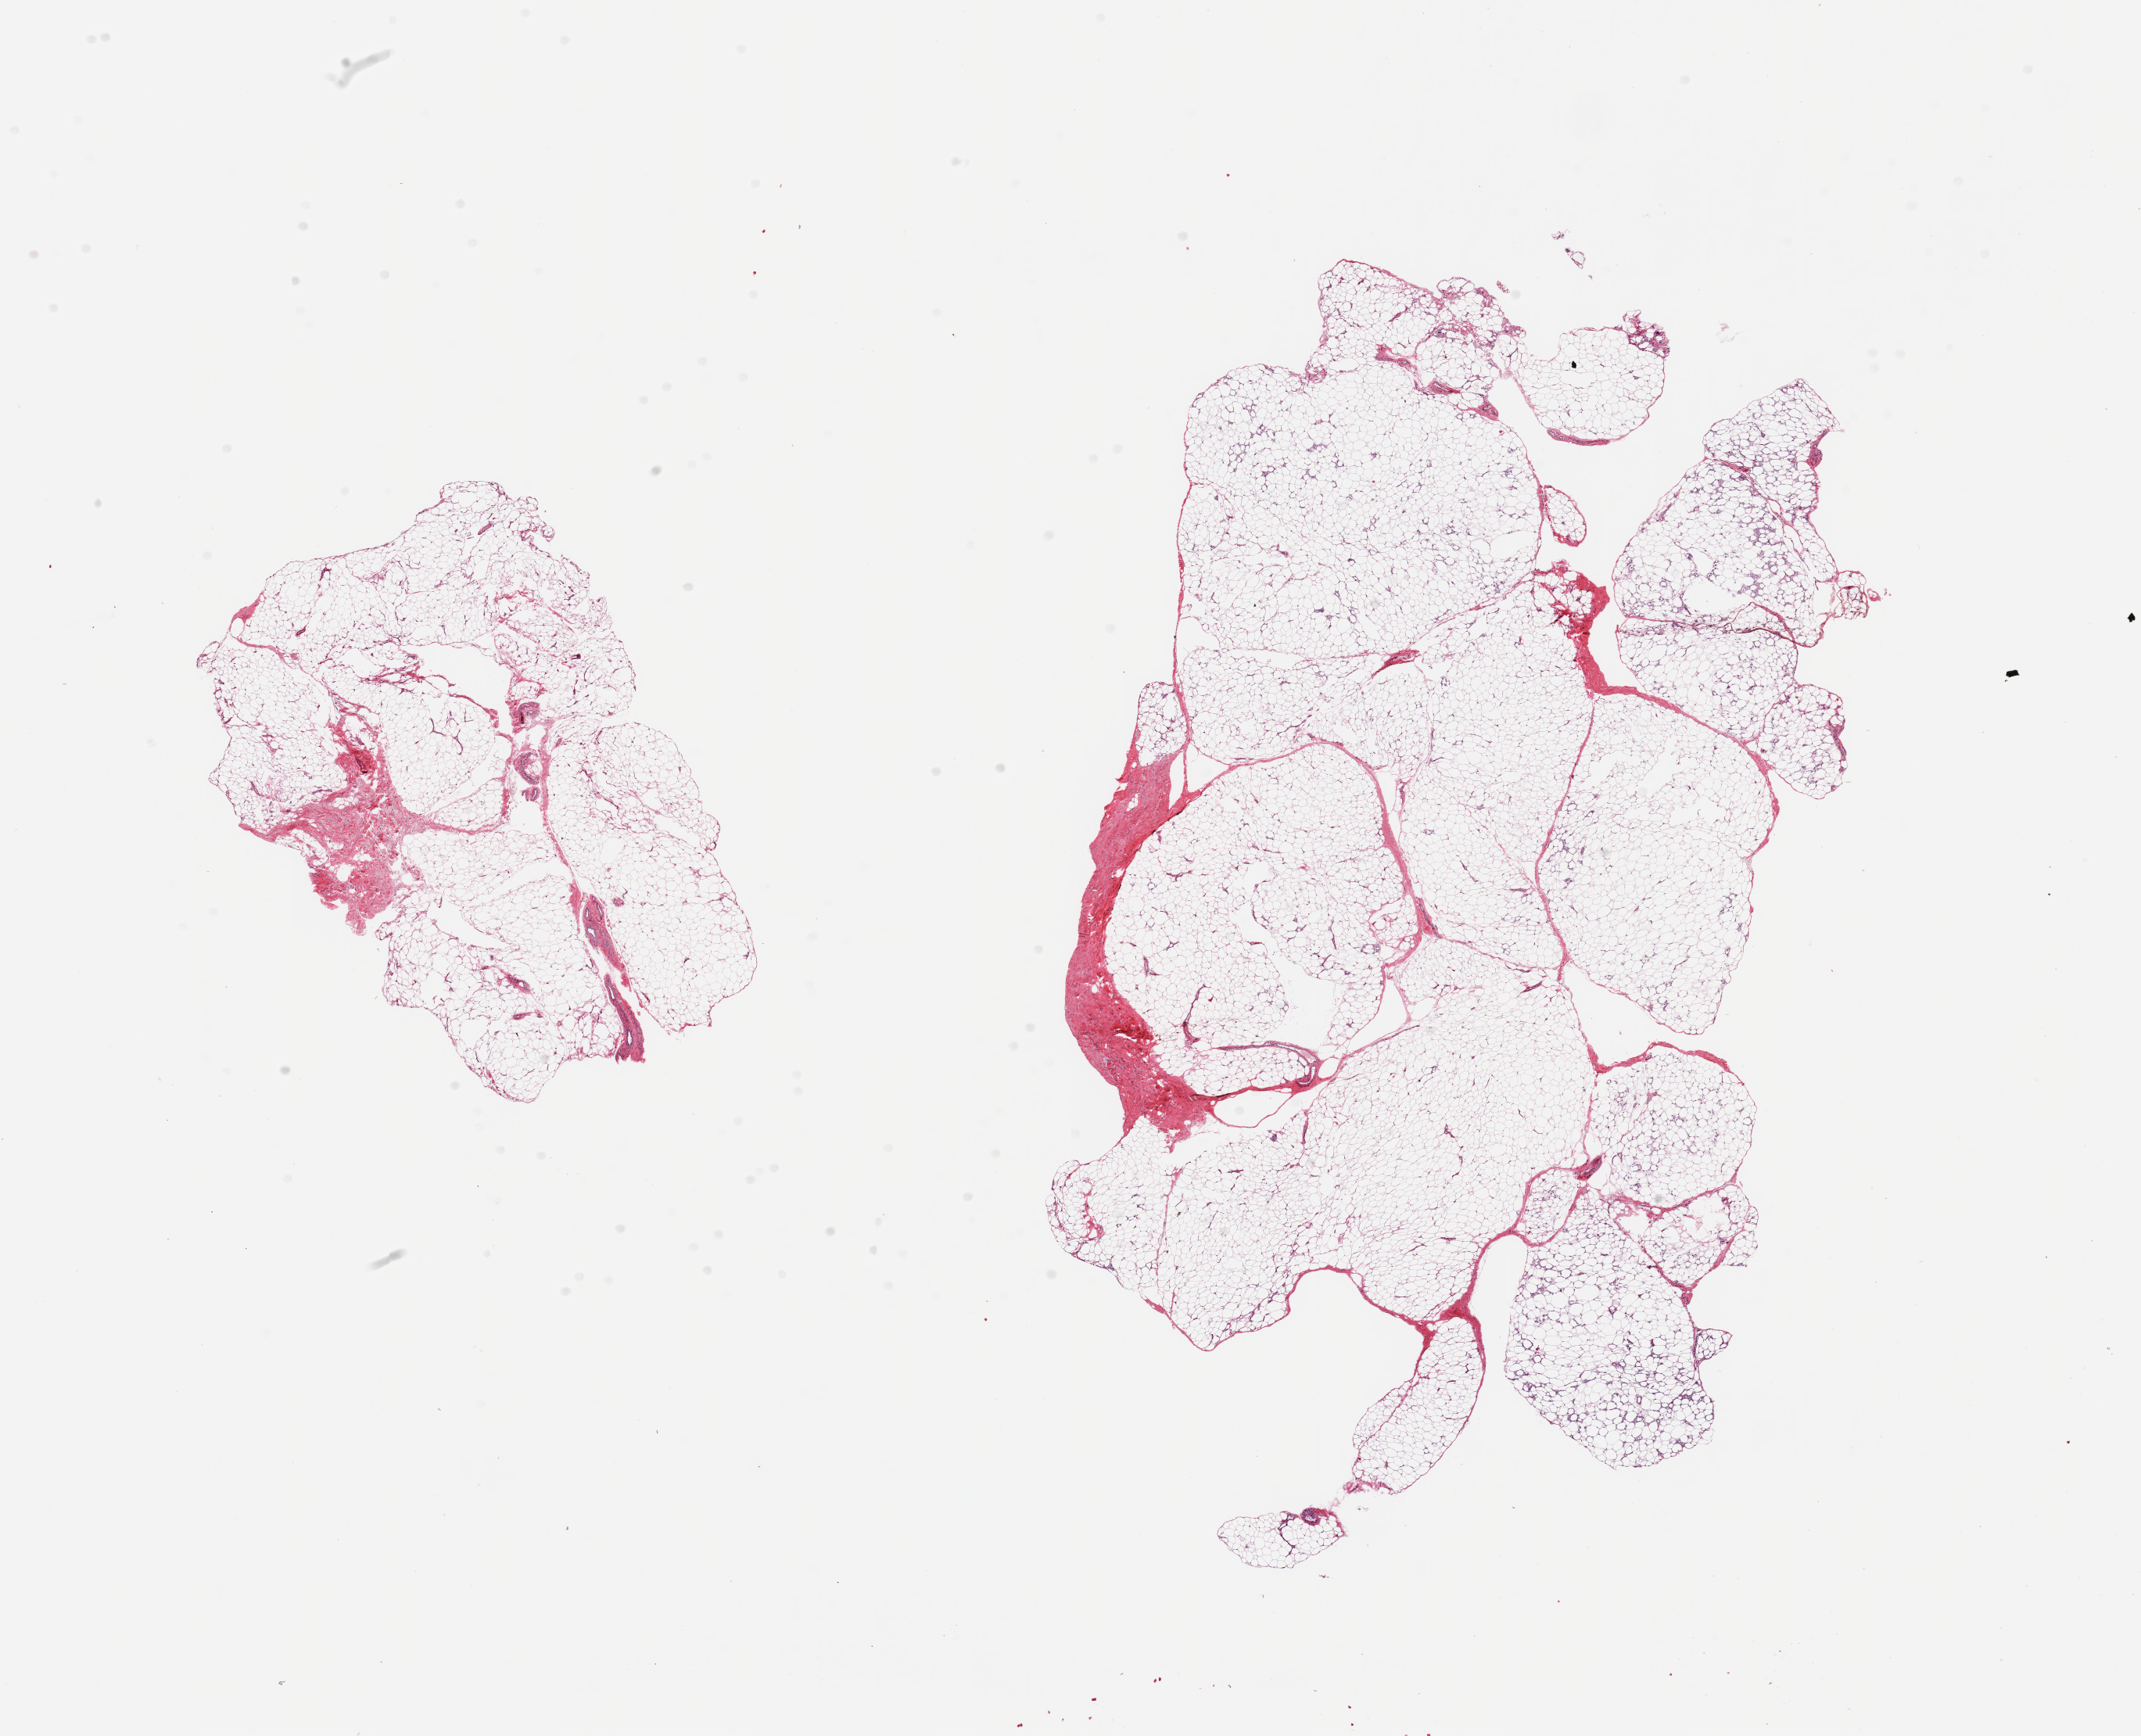
Whole-slide image, hematoxylin and eosin (H&E) stain, a low-resolution overview of the entire scanned area, about 21.7 x 17.6 mm. PAXgene-fixed, paraffin-embedded tissue. Section of adipose tissue (target tissue). Tissue donor sample. Donor sex: male.
Pathologist's review note for this sample: 2 pieces; Fascia/vasuclar elements are <10% of tissue.